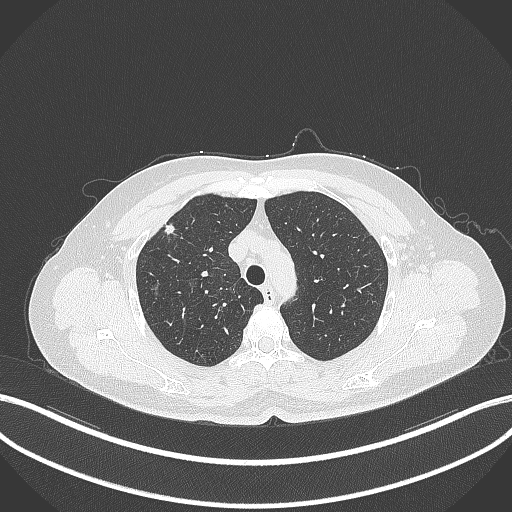
Chest CT, one axial slice; lung window (W 1500 / L -600 HU); 1 mm slice thickness; 512 × 512 image matrix, field of view 400 × 400 mm. Female patient, age 56 years. From the clinical record (not read from this slice): clinical TNM (as recorded): T1c N0 M0.
Outlined on this slice (bounding box drawn by a radiologist):
- lung tumour (recorded histology: adenocarcinoma): bounding box <162,220,180,238> (left, top, right, bottom; pixels)